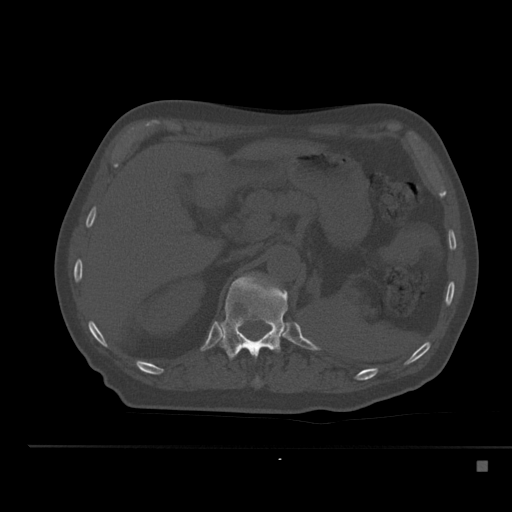
CT including the spine, one axial slice. Slice 229 of 517 in the series (ordered by position). Reconstruction kernel Br40s. 120 kVp. Bone window (W 1800 / L 400 HU). 1.5 mm slice thickness. 512 × 512 image matrix. Male patient, age 70 years. From the clinical record (not read from this slice): primary cancer: renal.
Annotated regions visible in this slice (semi-automatically segmented with operator editing):
- T11 vertebra: bounding box [x1, y1, x2, y2] px = [255, 377, 260, 385]
- T12 vertebra: [215, 275, 288, 360]